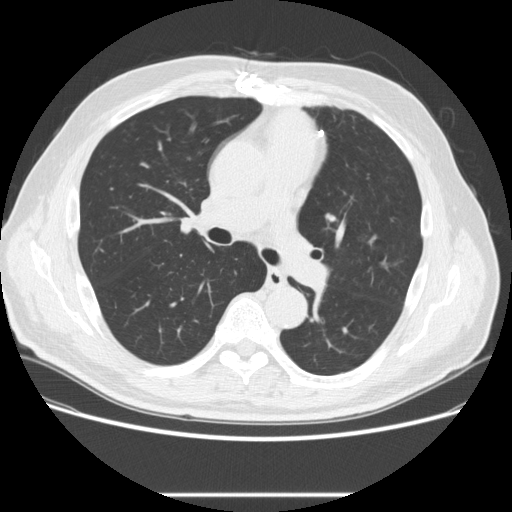
Low-dose screening chest CT, axial slice, second annual screen, lung window (W 1500 / L -600 HU), standard (soft-tissue) reconstruction kernel (STANDARD). Male participant, aged 66 years at enrolment. Former smoker at enrolment.
Lesion marked by an expert reader, bounding box <319,201,349,232> (left, top, right, bottom; pixels). The exam's reader record, not a measurement of the box and not confirmed to be the same lesion: non-calcified nodule or mass ≥4 mm, right lower lobe, 4 × 4 mm, smooth margins, soft tissue attenuation, pre-existing on the prior screen: yes; interval growth: no. Note: the box lies in the patient's left hemithorax on this image, whereas the reader's record names the right lung; they may be different findings. Official screen result: positive, no significant change: stable abnormalities potentially related to lung cancer, unchanged since the prior screening exam. Later outcome: lung cancer diagnosed 449 days after this screen (after the third annual screen) — squamous cell carcinoma, NOS, left upper lobe, poorly differentiated (G3), stage IA (AJCC 6th edition), 27 mm at pathology.